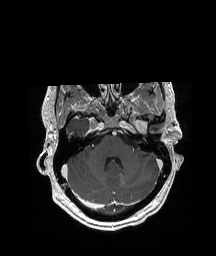
Brain MRI from a brain-tumour surgery series, one axial slice; position 146 of 208 along the scan axis; T1-weighted post-contrast; 1 mm slice thickness; 216 × 256 image matrix, field of view 228 × 270 mm. From the clinical record (not read from this slice): histopathology: Glioblastoma; WHO grade: 4; IDH mutation: no; tumour location: Left Anterior/Superior Temporal.
Outlined on this slice (expert manual segmentation):
- tumour: bounding box <123,114,158,127> (left, top, right, bottom; pixels)